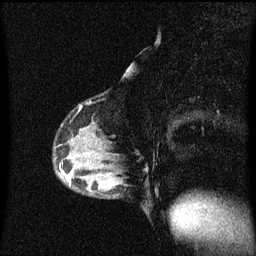
Breast MRI (dynamic contrast-enhanced), one sagittal slice. Dynamic contrast-enhanced series, image 2 of 3 at this slice position (ordered by acquisition). 1.5 T. TE 4.2 ms, TR 8.4 ms. 2 mm slice thickness. 256 × 256 image matrix, field of view 200 × 200 mm. Female patient, age 40 years.
Structures marked on this image (semi-automatically segmented with operator editing):
- analysis volume of interest (the breast-tissue region the enhancement analysis was run in; not a lesion): bounding box <82,172,125,199> (left, top, right, bottom; pixels)
- tumour enhancement mask (voxels above the 70 % enhancement threshold inside the analysis volume of interest): <97,178,104,187>